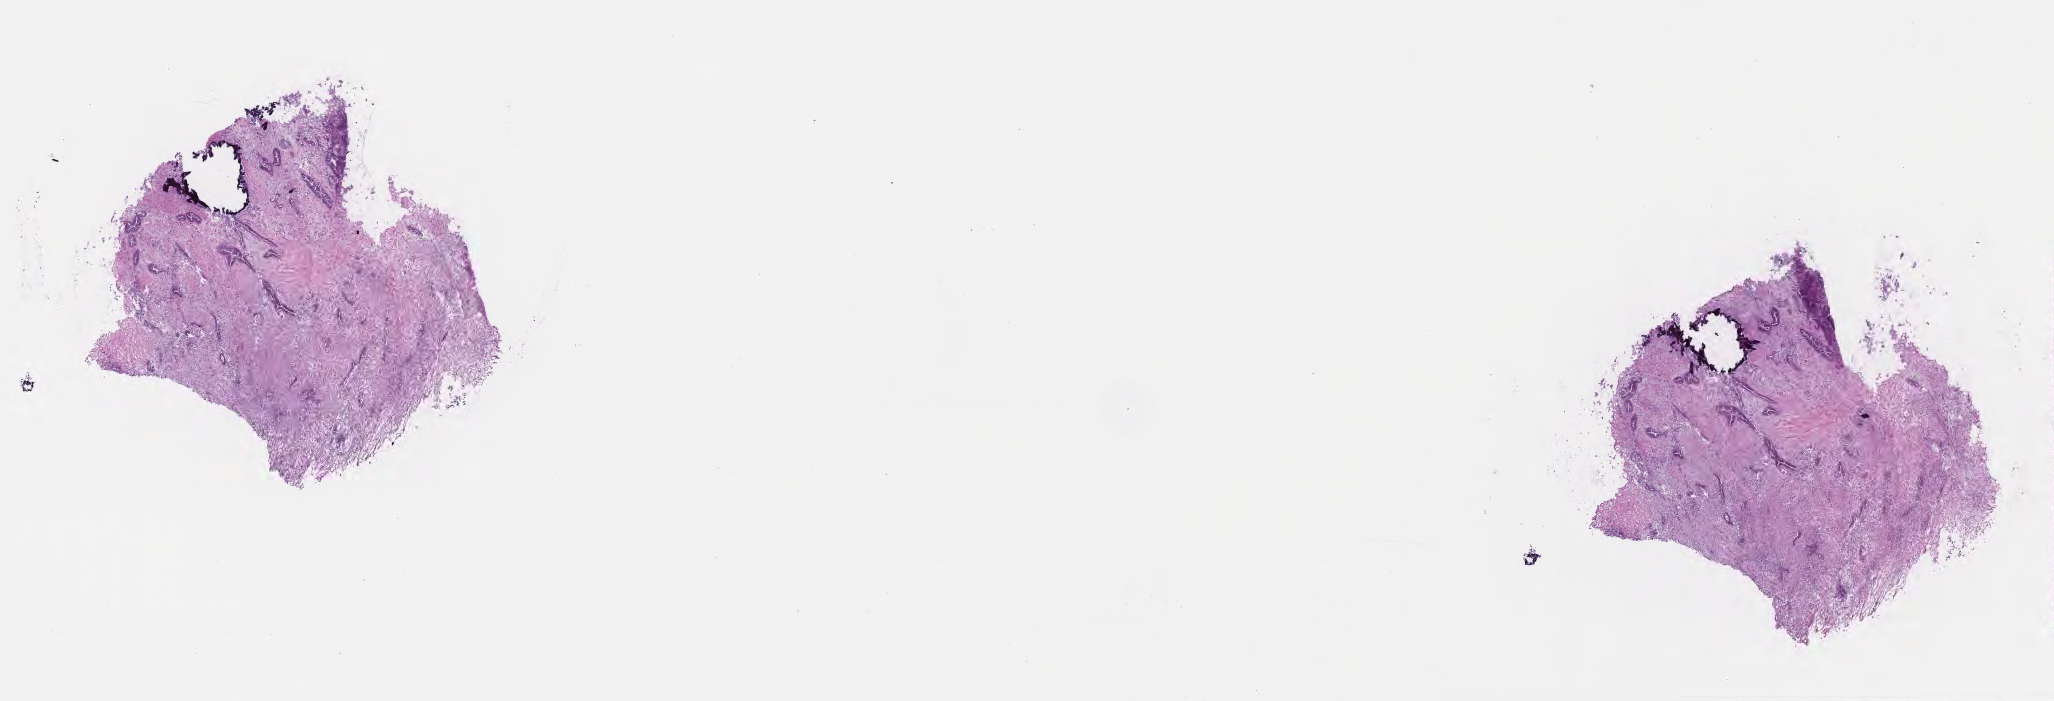
H&E whole-slide image, whole scanned area (about 16.6 x 5.7 mm) shown as a low-resolution overview. Frozen section. Primary tumor. Site: neck of pancreas. Female patient; age at initial diagnosis 80 years. Tumor grade: G2 (moderately differentiated). Pathologist review of this section (percent, as recorded): tumor cells 70%, tumor nuclei 70%, stromal cells 25%, necrosis 0%, normal cells 5%. Infiltration values recorded for this section: lymphocyte infiltration 7%, monocyte infiltration 3%, neutrophil infiltration 8%.
AJCC pathologic stage: Stage IIB. Section: bottom of the tissue portion. Histologic diagnosis: Infiltrating duct carcinoma, NOS.